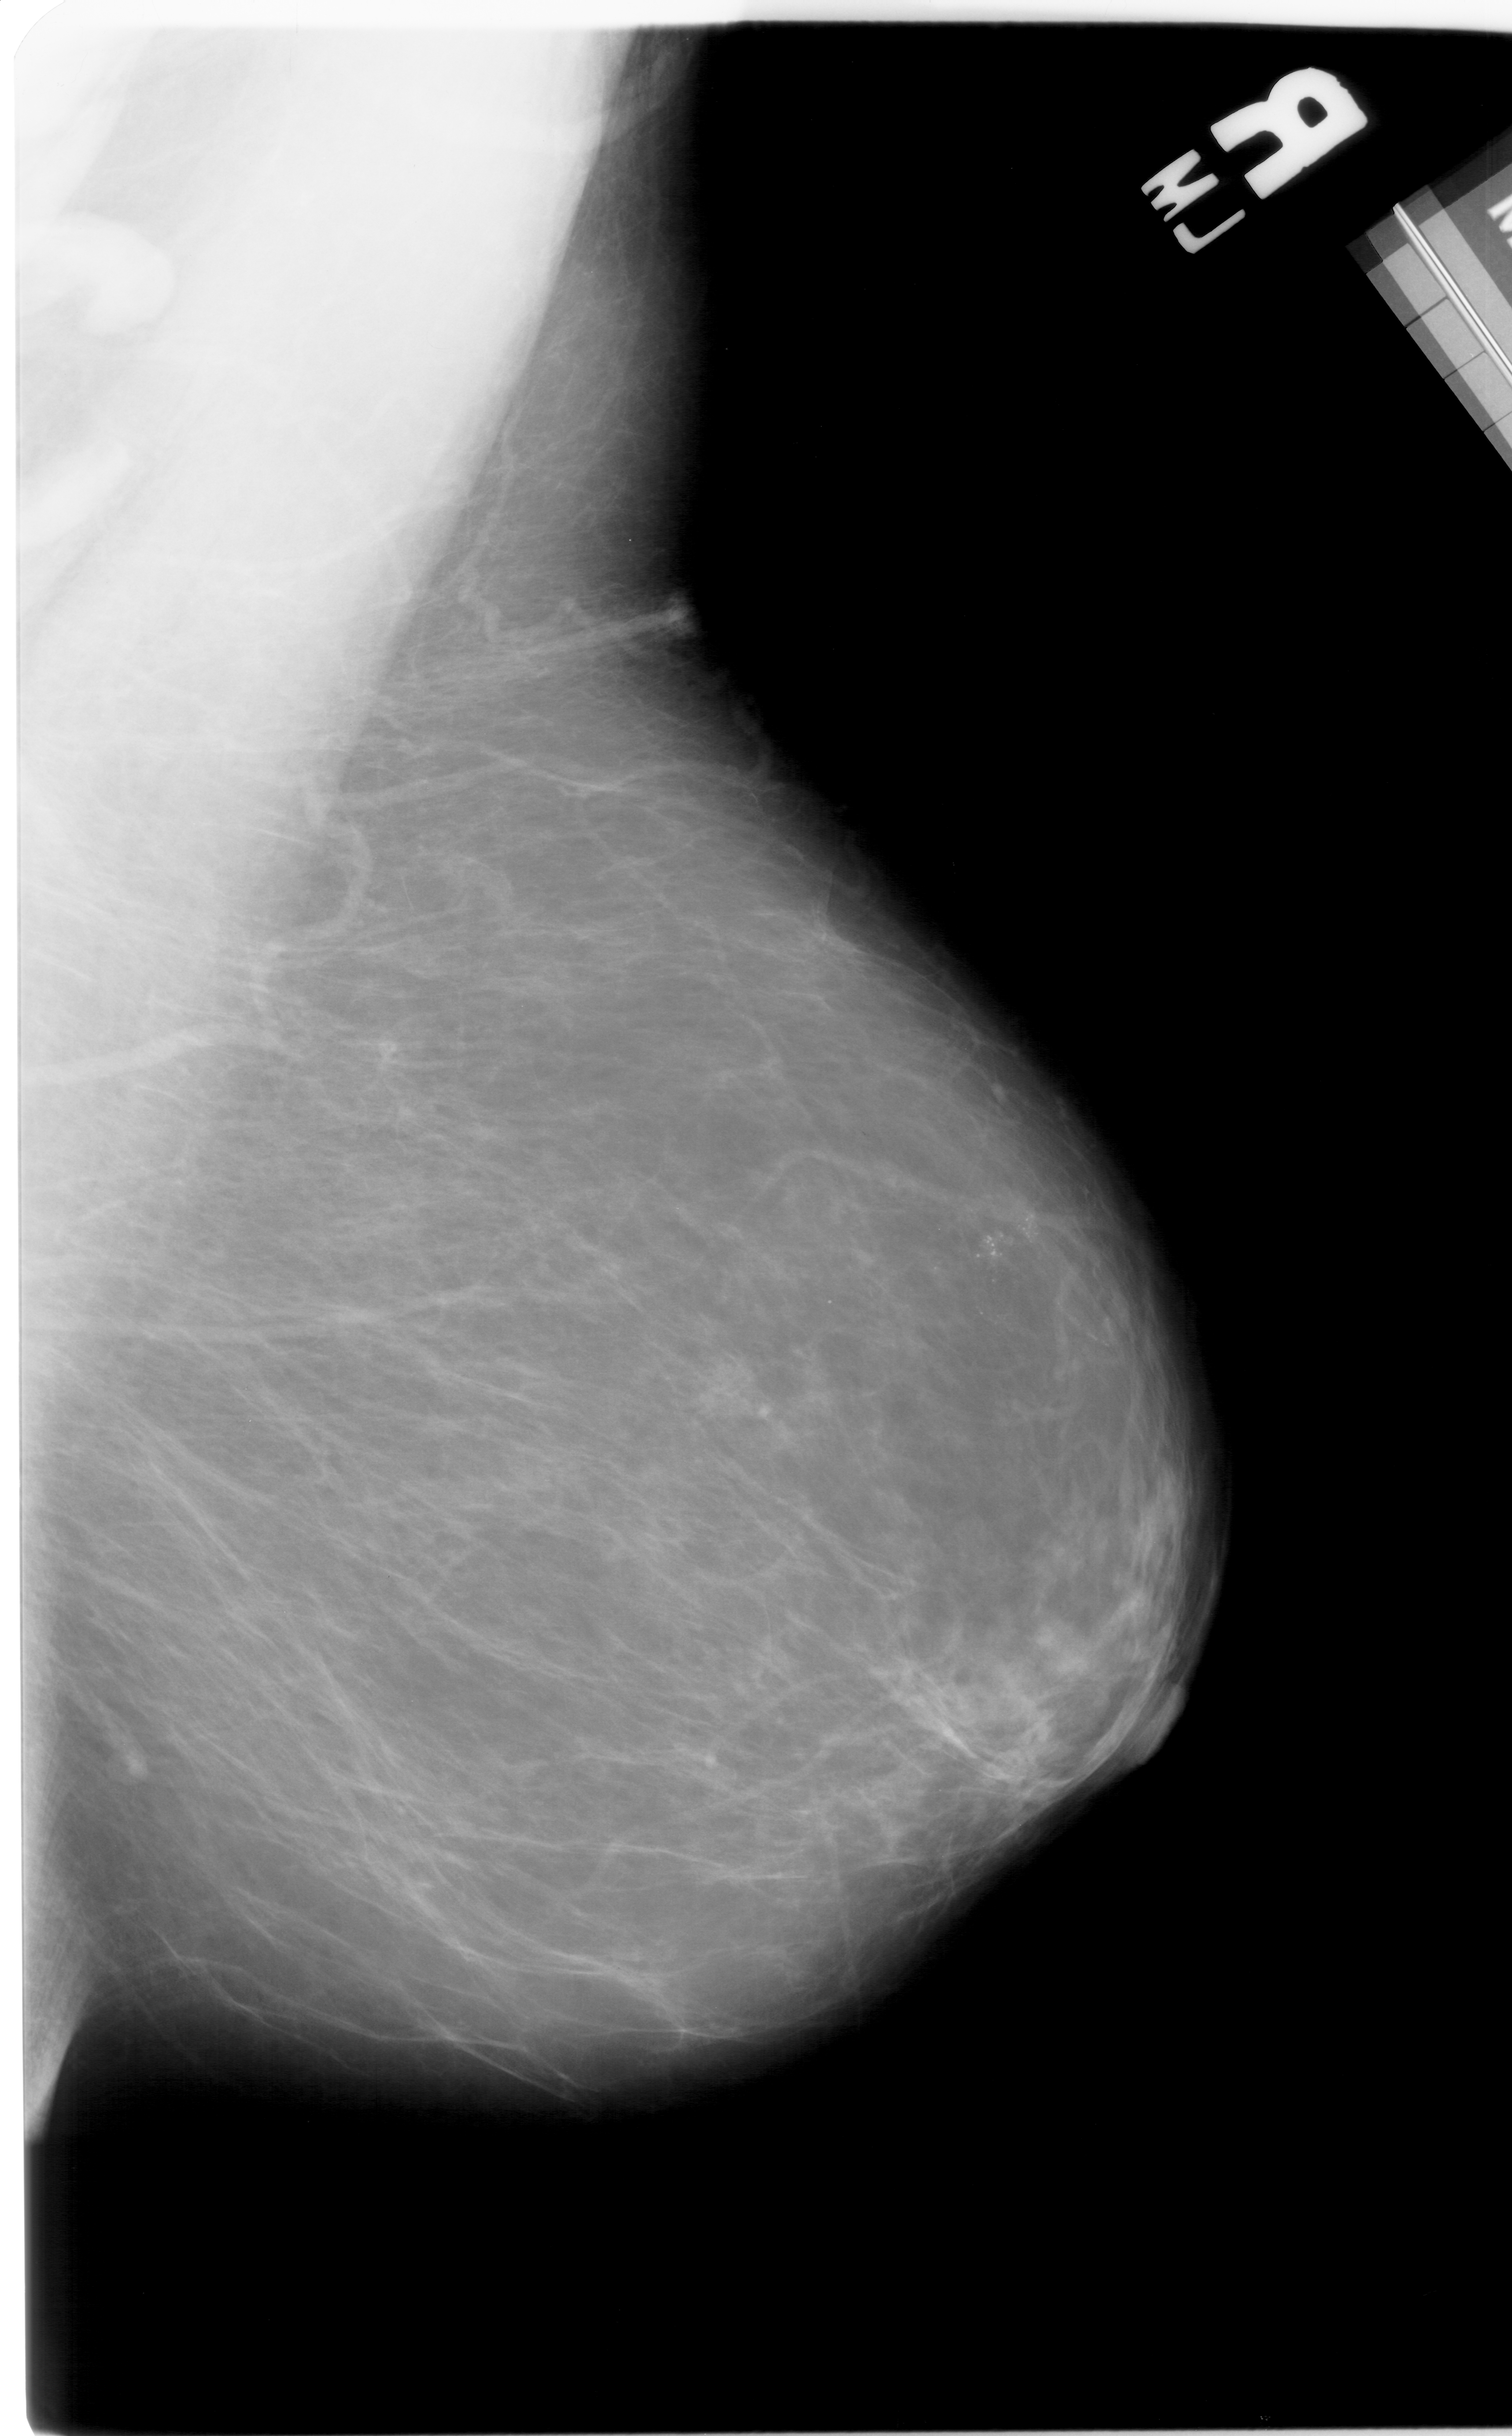
Digitized screen-film mammogram. Right breast. Mediolateral oblique (MLO) view. BI-RADS breast density category 2 (scale 1–4). 1512 × 2436 image matrix.
Marked abnormalities (boxes around the expert regions of interest):
- calcifications, morphology pleomorphic, distribution segmental; BI-RADS assessment category 4; subtlety rating 4 on a 1 (subtle) to 5 (obvious) scale; pathology result (as recorded, not read from the image): malignant: bounding box (x1, y1, x2, y2) in pixels: (898, 1194, 1027, 1346)